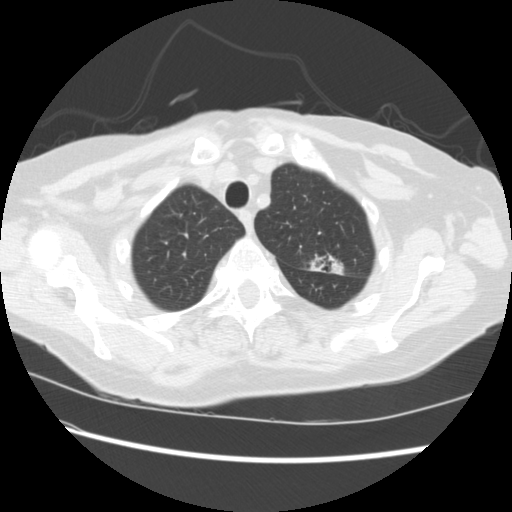
Low-dose screening chest CT, axial slice. First (baseline) screen. Lung window (W 1500 / L -600 HU). Standard (soft-tissue) reconstruction kernel (STANDARD). Slice 40 of 224 in the series. 512 × 512 image matrix, field of view 340 × 340 mm. Female participant, aged 74 years at enrolment. Former smoker at enrolment.
• Expert reader's lesion annotation, bounding box (x1, y1, x2, y2) in pixels: (297, 245, 347, 283).
• The screening reader recorded 2 non-calcified nodules or masses ≥4 mm on this exam (left upper lobe, right lower lobe); which of them this box marks is not recorded.